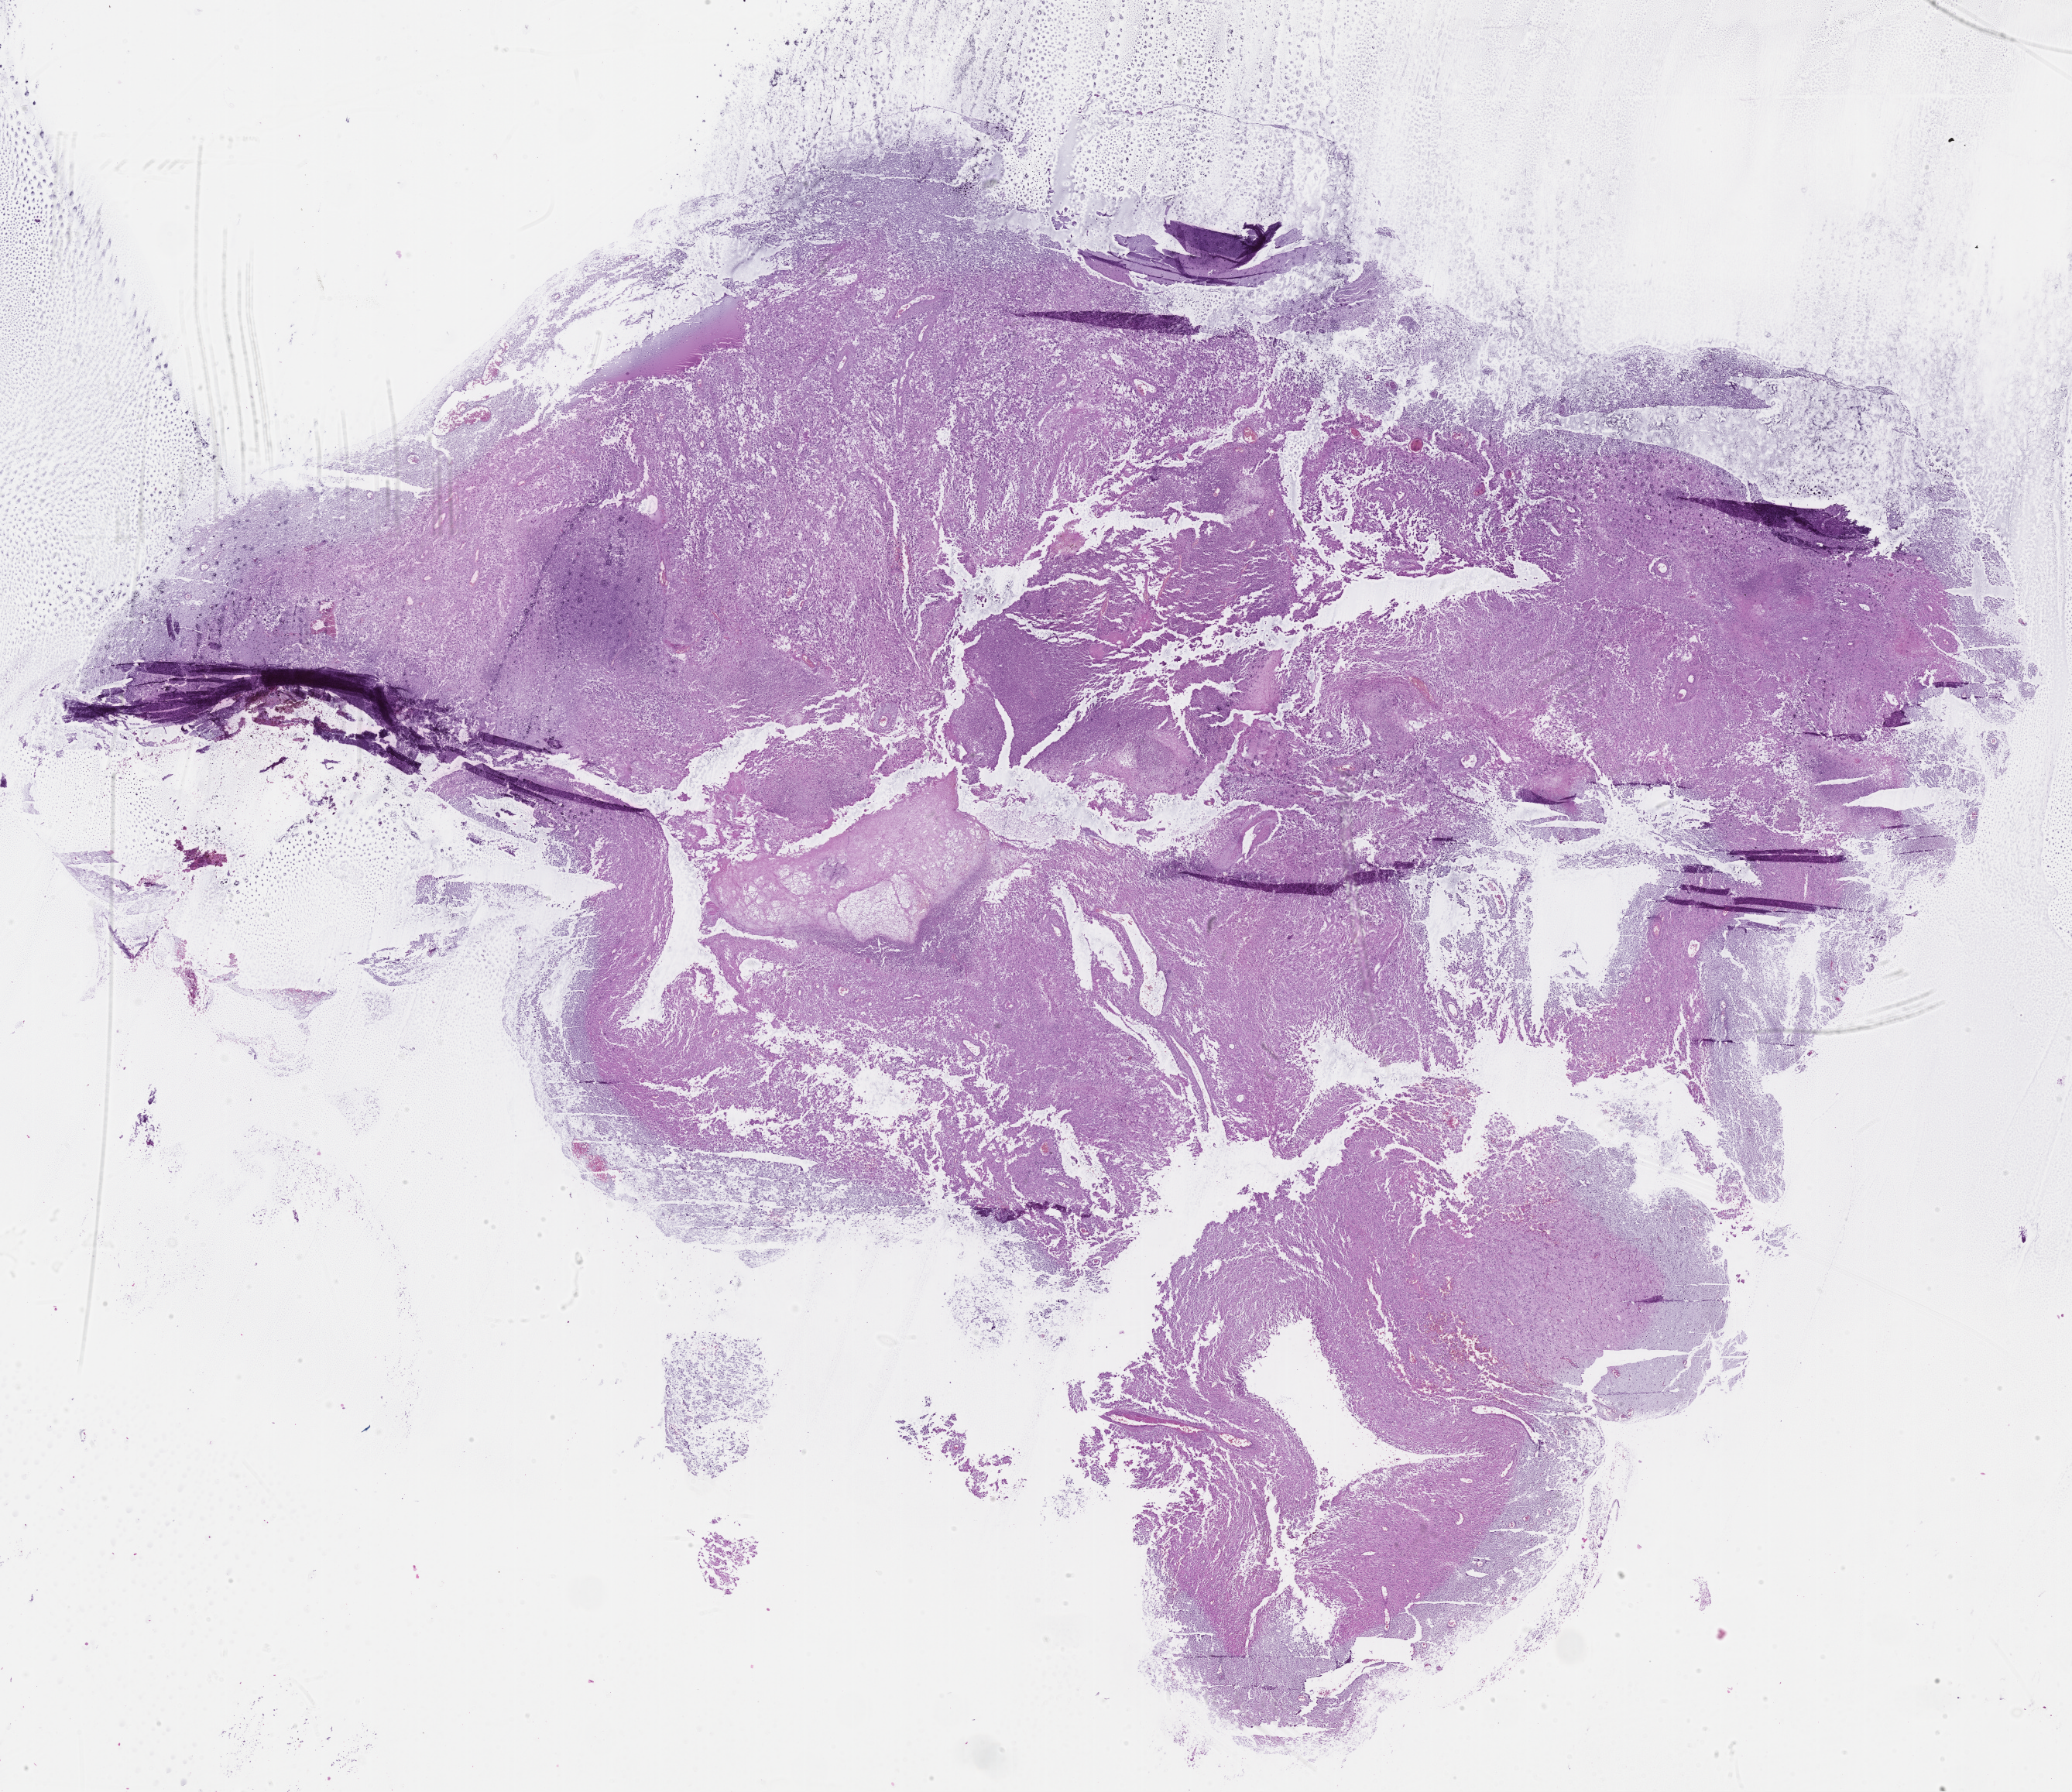
Whole-slide histology image, H&E-stained — whole scanned area (about 21.7 x 18.8 mm) shown as a low-resolution overview, formalin-fixed paraffin-embedded (FFPE) diagnostic section, primary tumour sample from the brain. Male patient; age at initial diagnosis 61 years.
- pathologic diagnosis: Glioblastoma